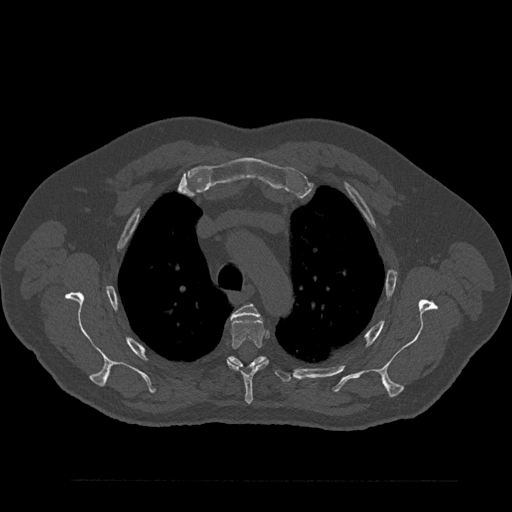
CT including the spine, one axial slice. Reconstruction kernel Br40s/3. Bone window (W 1800 / L 400 HU). 0.5 mm slice thickness. 512 × 512 image matrix, field of view 430 × 430 mm. Male patient, age 61 years. Case-level facts recorded for this patient, not image findings: primary cancer: prostate.
Outlined on this slice (semi-automatically segmented with operator editing):
- T3 vertebra: box from (x=230, y=304) to (x=259, y=318) px
- T4 vertebra: (x=227, y=318)–(x=269, y=404)
- T5 vertebra: (x=228, y=356)–(x=291, y=382)